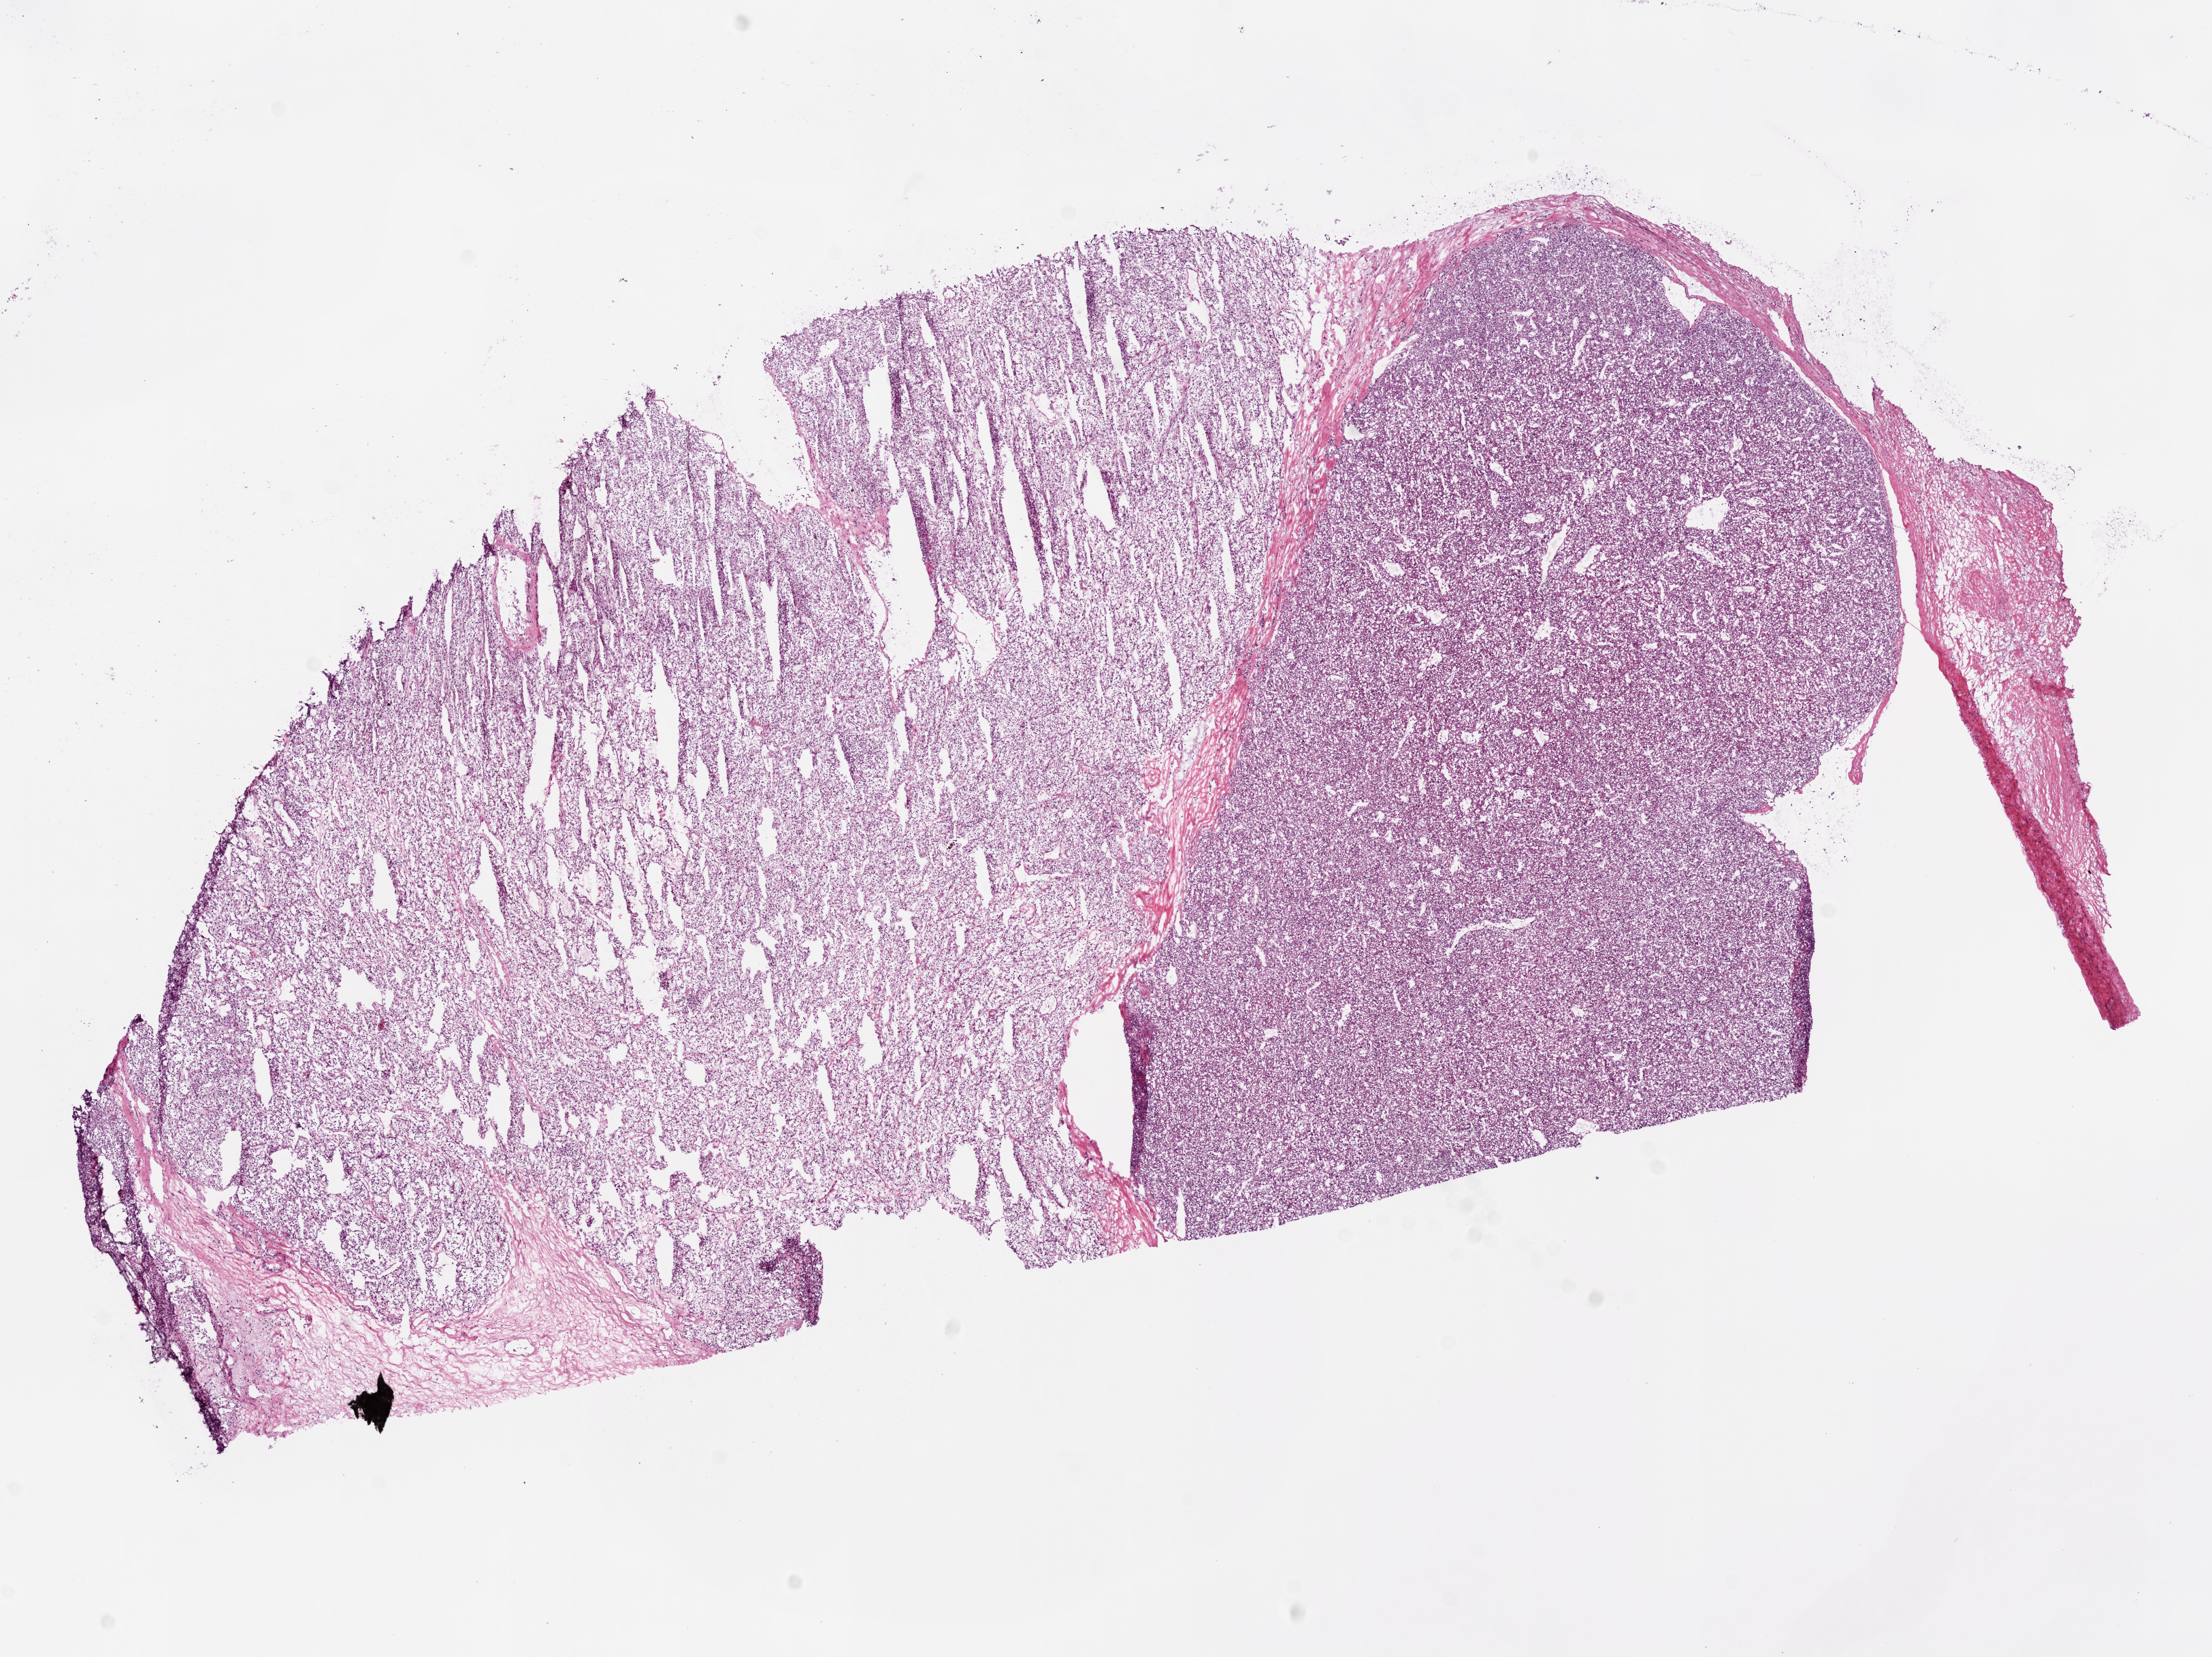
Whole-slide histology image, Hematoxylin and eosin (H&E) stained, a low-resolution overview of the entire scanned area, about 13.0 x 9.8 mm. Frozen section. Primary tumour sample from the kidney. Male, age 57 years at initial diagnosis. Histologic grade: G2 (moderately differentiated). Pathologist review of this section (percent, as recorded): tumour cells 90%, tumour nuclei 85%, normal cells 0%, stromal cells 10%, necrosis 0%.
AJCC pathologic stage: I. Diagnosis: Clear cell adenocarcinoma, NOS.